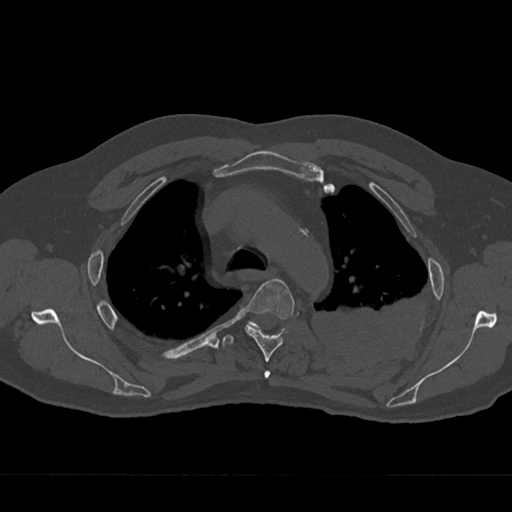
CT including the spine, one axial slice; slice 514 of 797 in the series (ordered by position); reconstruction kernel Br40s/3; bone window (W 1800 / L 400 HU); 0.5 mm slice thickness; 512 × 512 image matrix. Patient: male, 75 years. From the clinical record (not read from this slice): primary cancer: renal; vertebrae with lytic lesions (as recorded): T4.
Structures marked on this image (semi-automatically segmented with operator editing):
- T3 vertebra: bounding box [x1, y1, x2, y2] px = [264, 371, 271, 378]
- T4 vertebra: [245, 278, 294, 362]
- T5 vertebra: [222, 321, 284, 347]